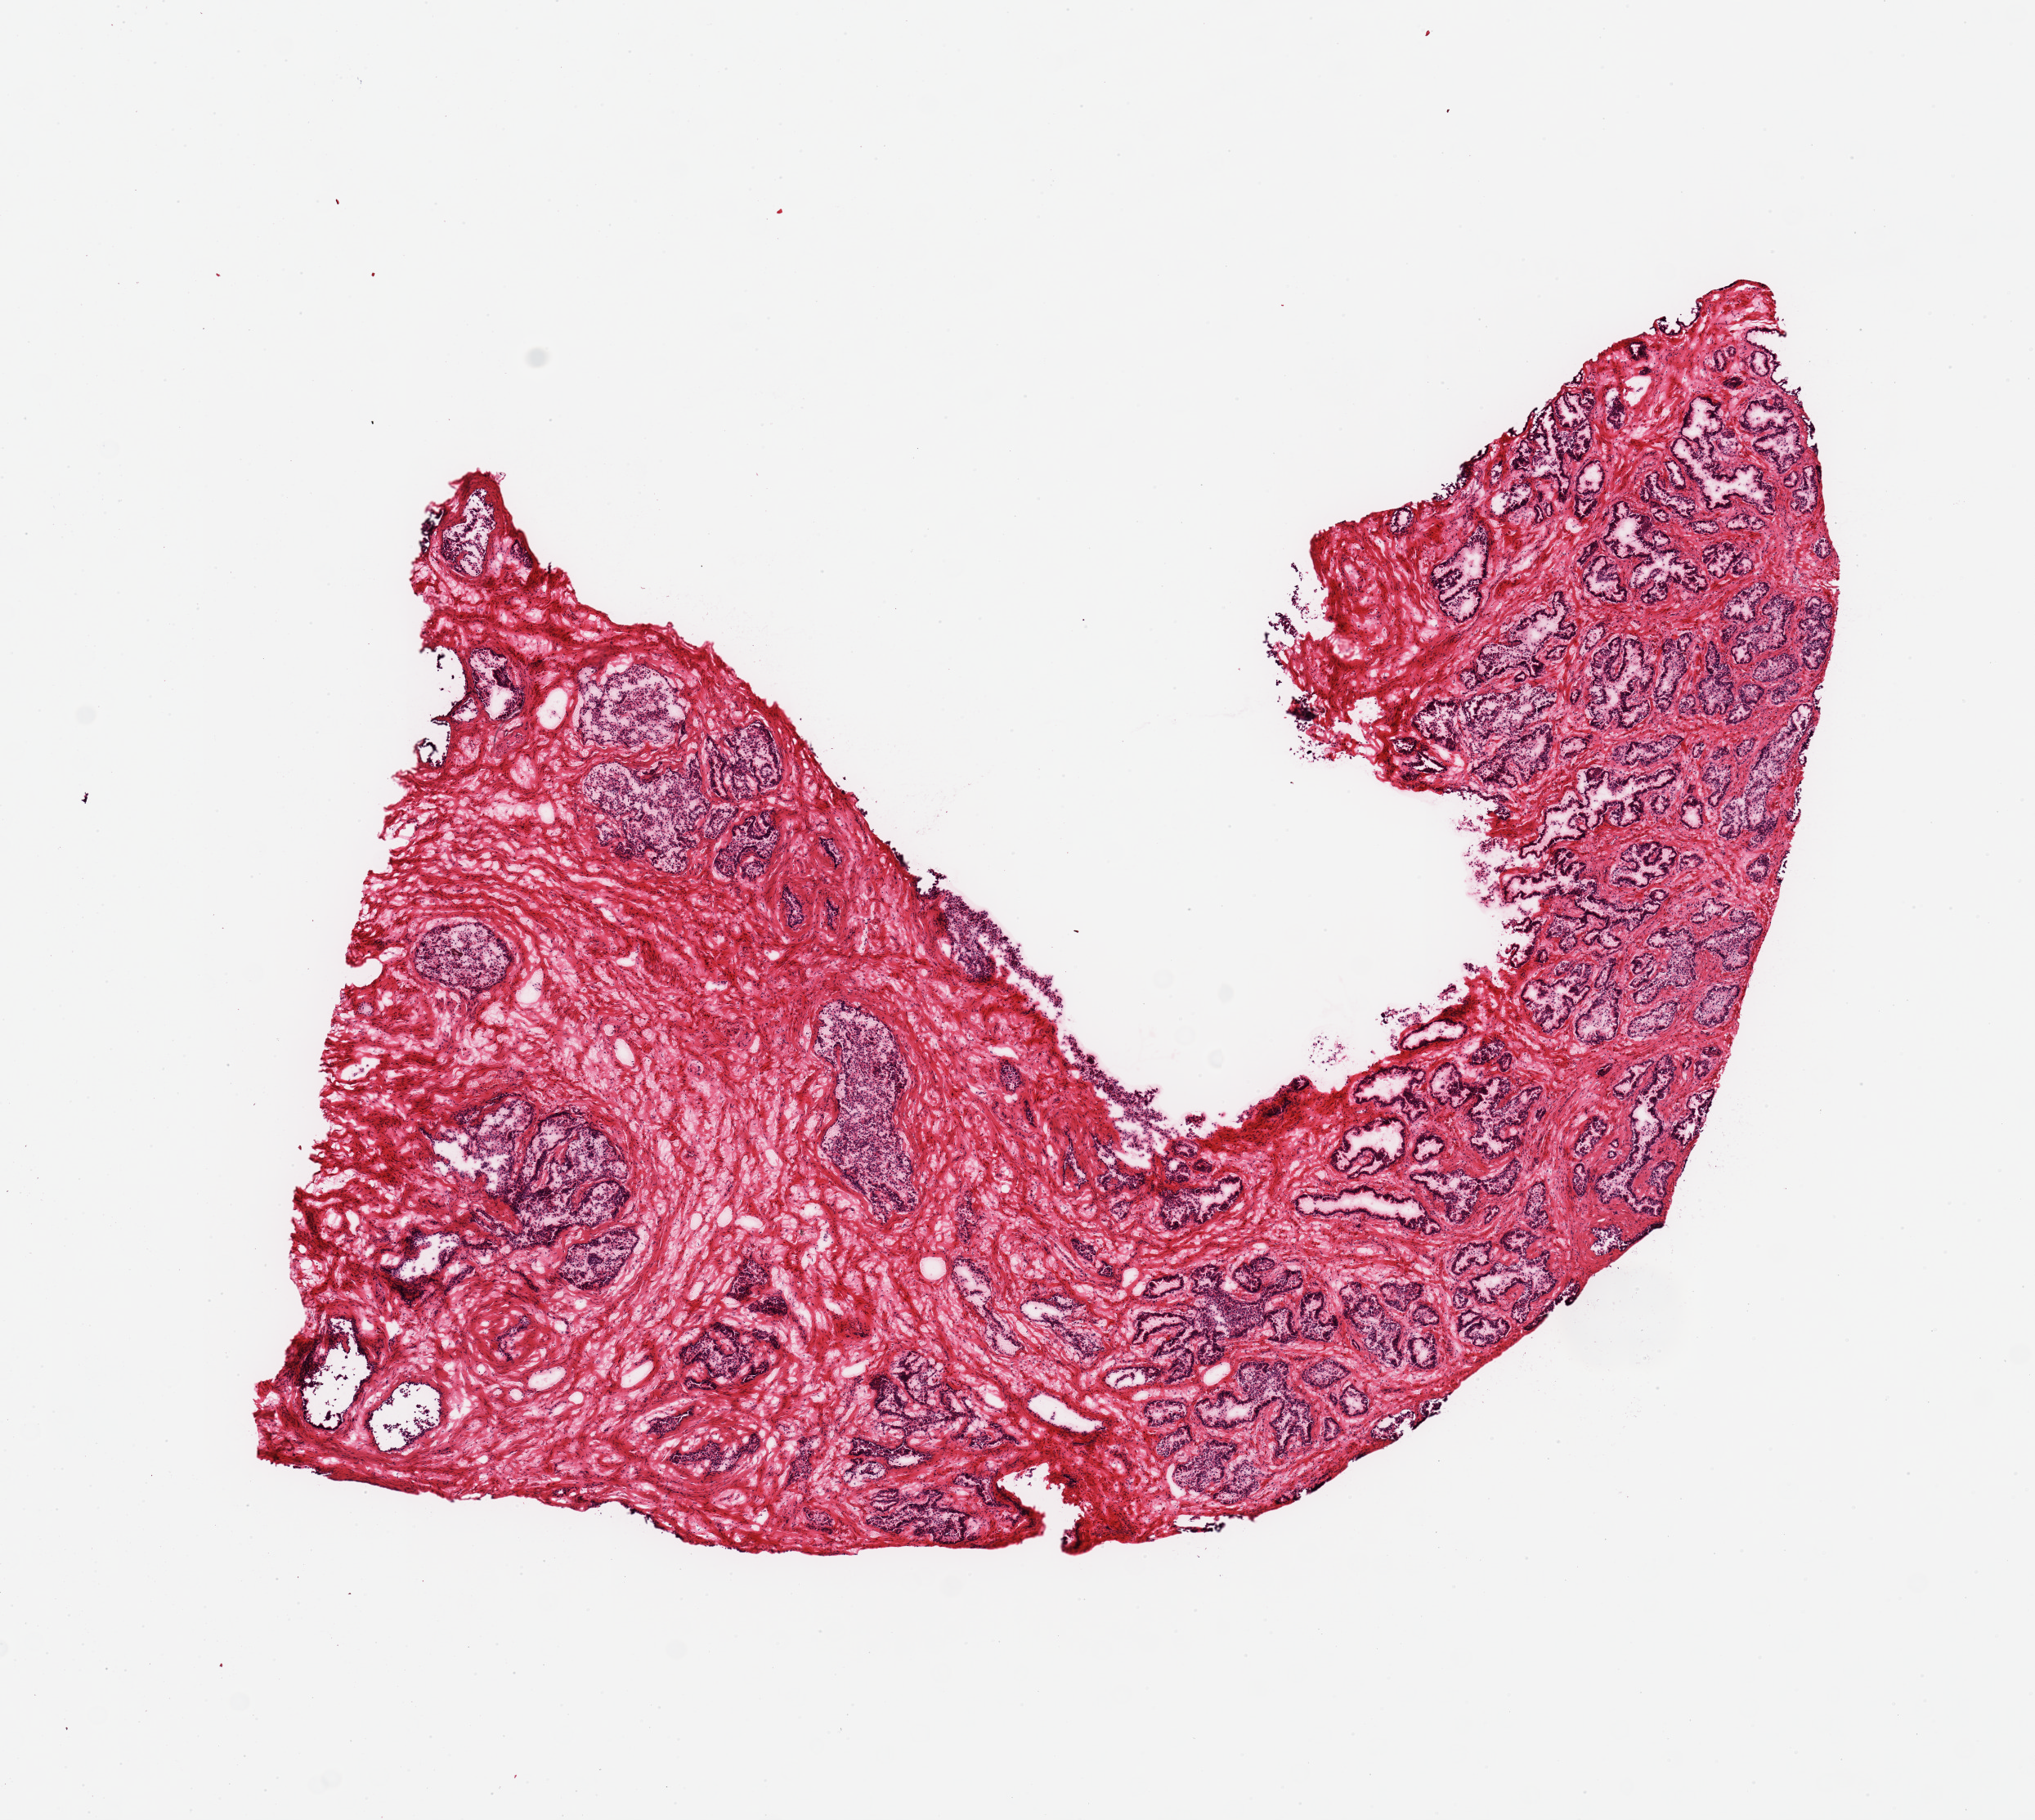
H&E whole-slide image, a low-resolution overview of the entire scanned area, about 9.8 x 8.8 mm; frozen section; target tissue: prostate; donor tissue sample.
Reviewer comment on this tissue sample: 1 piece; acini present throughout.